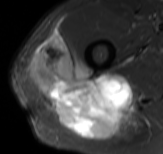
MRI of an extremity soft-tissue mass, one axial slice; STIR; MR volume resampled by the dataset authors to the PET/CT grid (not the native acquisition matrix); 3.27 mm slice thickness; 163 × 154 image matrix, field of view 159 × 150 mm. Male patient. From the clinical record (not read from this slice): histological type: poorly differentiated synovial sarcoma; grade: high; site of the primary tumour: right buttock.
Annotated regions visible in this slice (expert contour drawn on MRI and transferred to this co-registered scan by the dataset authors):
- gross tumour volume including surrounding oedema: bounding box (x1, y1, x2, y2) in pixels: (27, 32, 145, 140)
- gross tumour volume (mass): (29, 32, 133, 140)